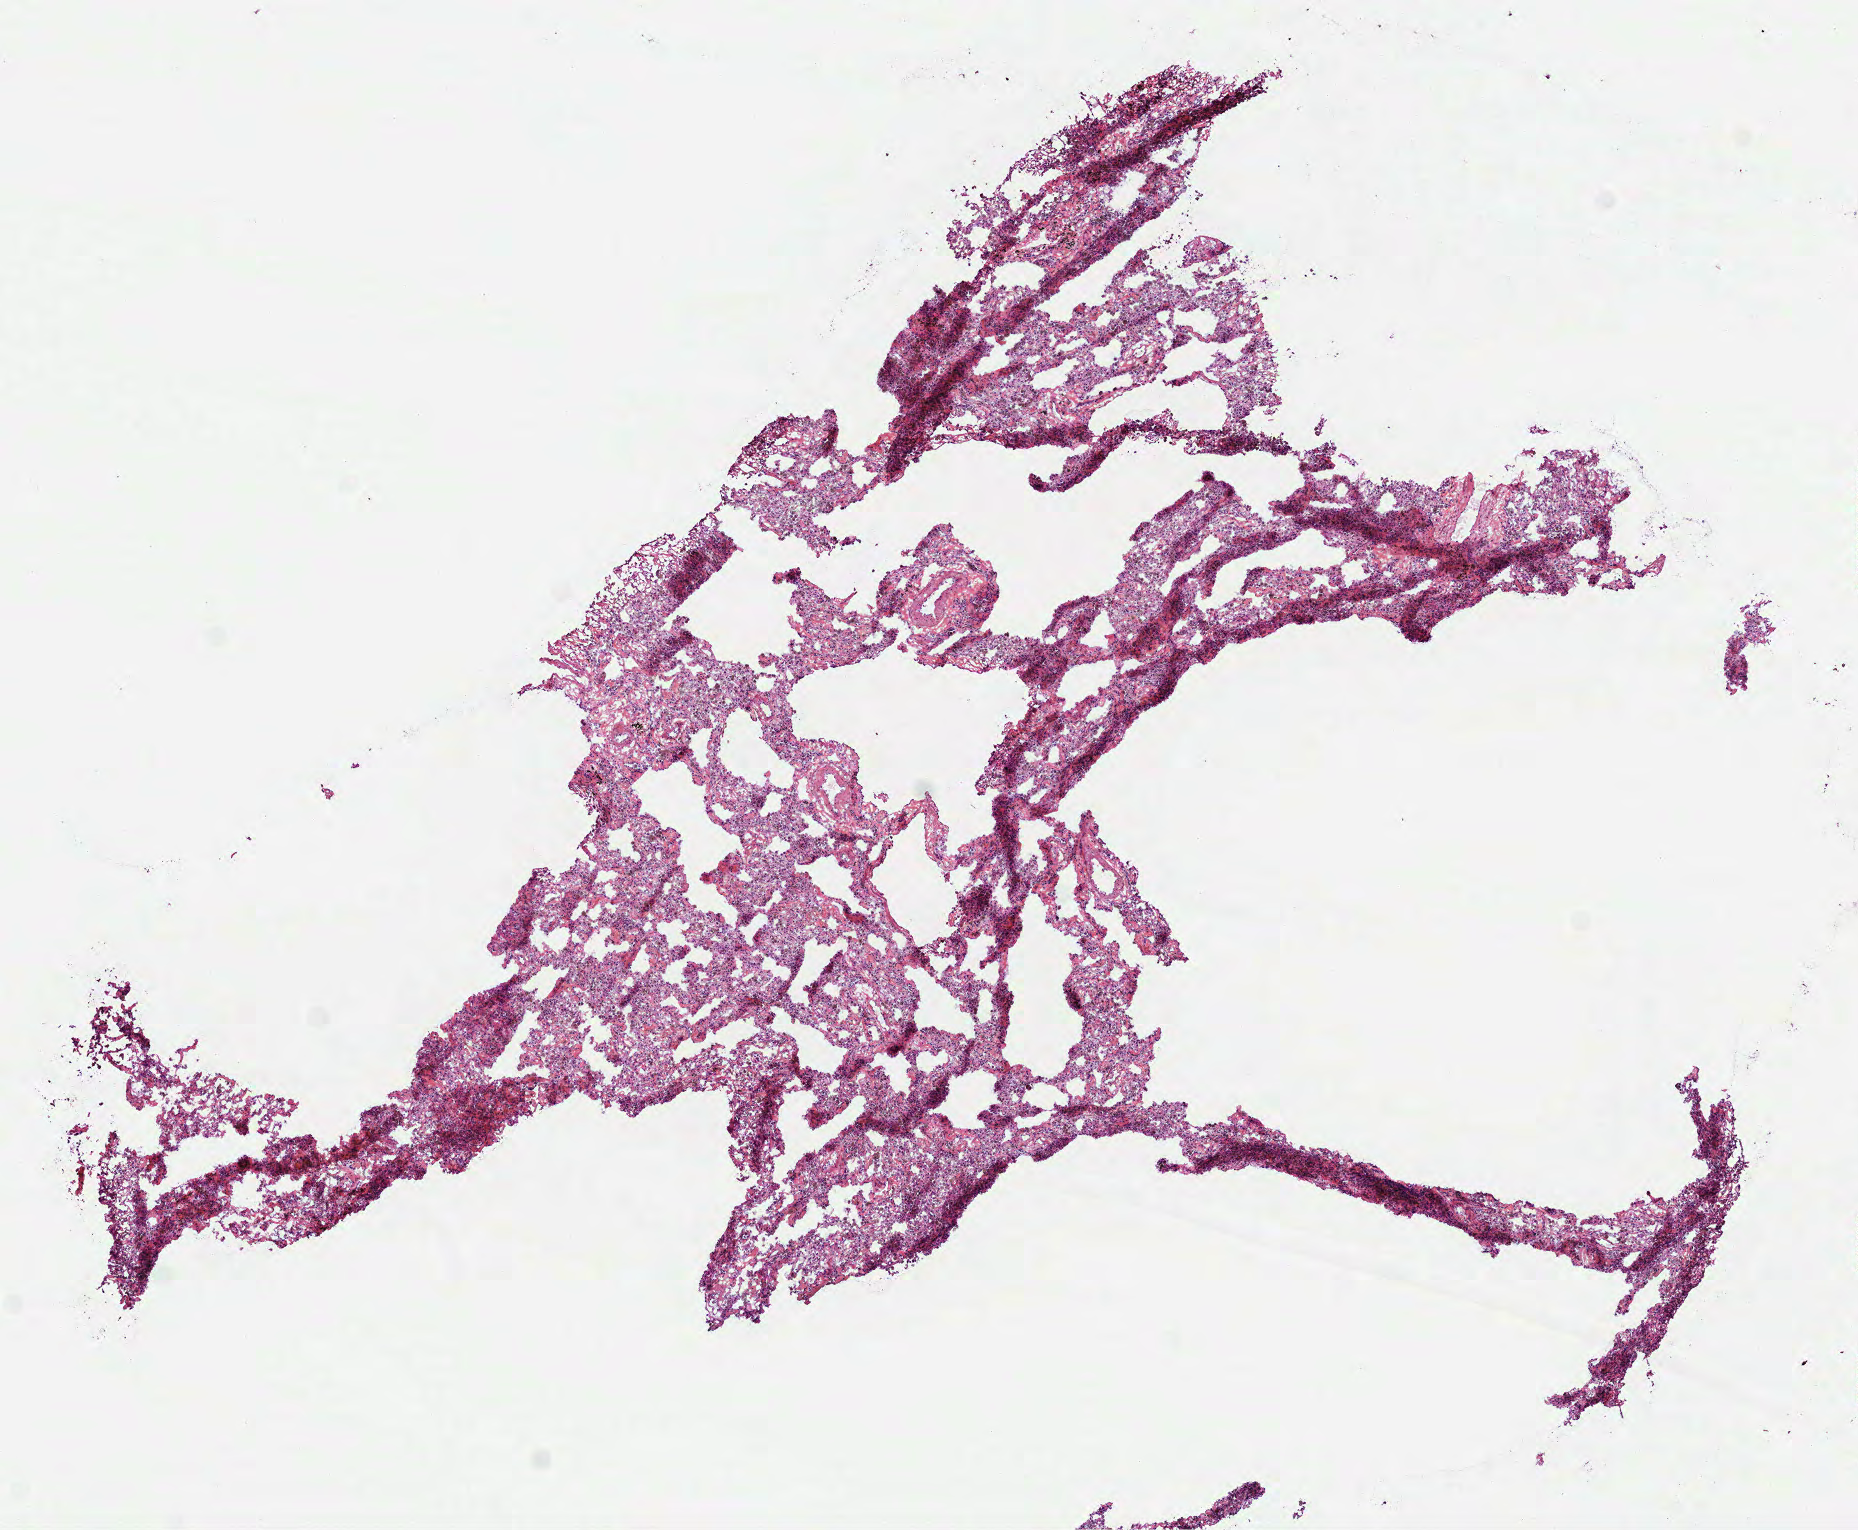
Digitized H&E tissue section (whole slide) — a low-resolution overview of the entire scanned area, about 7.5 x 6.2 mm (slide scanned at 40x); frozen section; sample: solid tissue normal (non-tumour tissue), lung. Male patient; age at initial diagnosis 60 years.
• this section: solid tissue normal sample (biorepository sample class)
• patient diagnosis: Squamous cell carcinoma, NOS (upper lobe, lung)